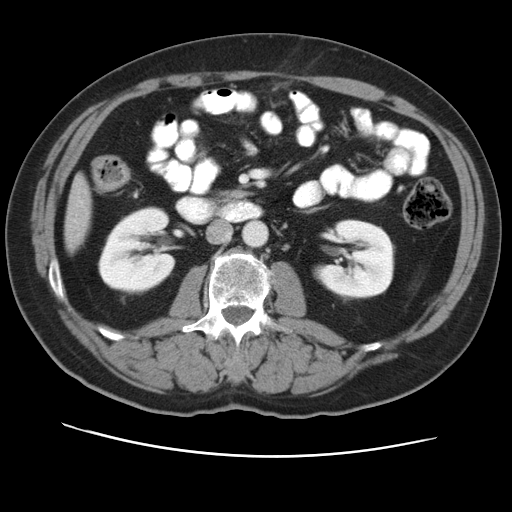
Contrast-enhanced abdominal CT, one axial slice; slice 14 of 49 in the series (ordered by position); reconstruction kernel STANDARD; soft-tissue window (W 400 / L 40 HU); 5 mm slice thickness; 512 × 512 image matrix. Male patient, age 59 years. From the clinical record (not read from this slice): diagnosis: colorectal cancer liver metastases, imaged before liver resection.
Annotated regions visible in this slice (outlined manually by an expert reader):
- liver: bounding box [x1, y1, x2, y2] px = [65, 179, 91, 250]
- planned liver remnant (the part of the liver to remain after resection): [70, 179, 91, 212]